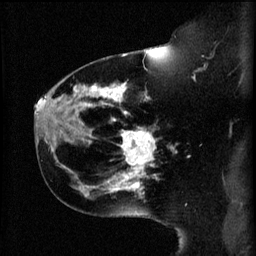
Breast MRI (dynamic contrast-enhanced), one sagittal slice; 3 images stored at this slice position (order not interpretable as contrast timing); 1.5 T; TE 4.2 ms, TR 11 ms; 2 mm slice thickness; 256 × 256 image matrix, field of view 180 × 180 mm. Female patient, age 44 years.
Structures marked on this image (semi-automatic segmentation, software-assisted and operator-edited):
- analysis volume of interest (the breast-tissue region the enhancement analysis was run in; not a lesion): bounding box <114,128,159,179> (left, top, right, bottom; pixels)
- tumour enhancement mask (voxels above the 70 % enhancement threshold inside the analysis volume of interest): <120,130,157,179>